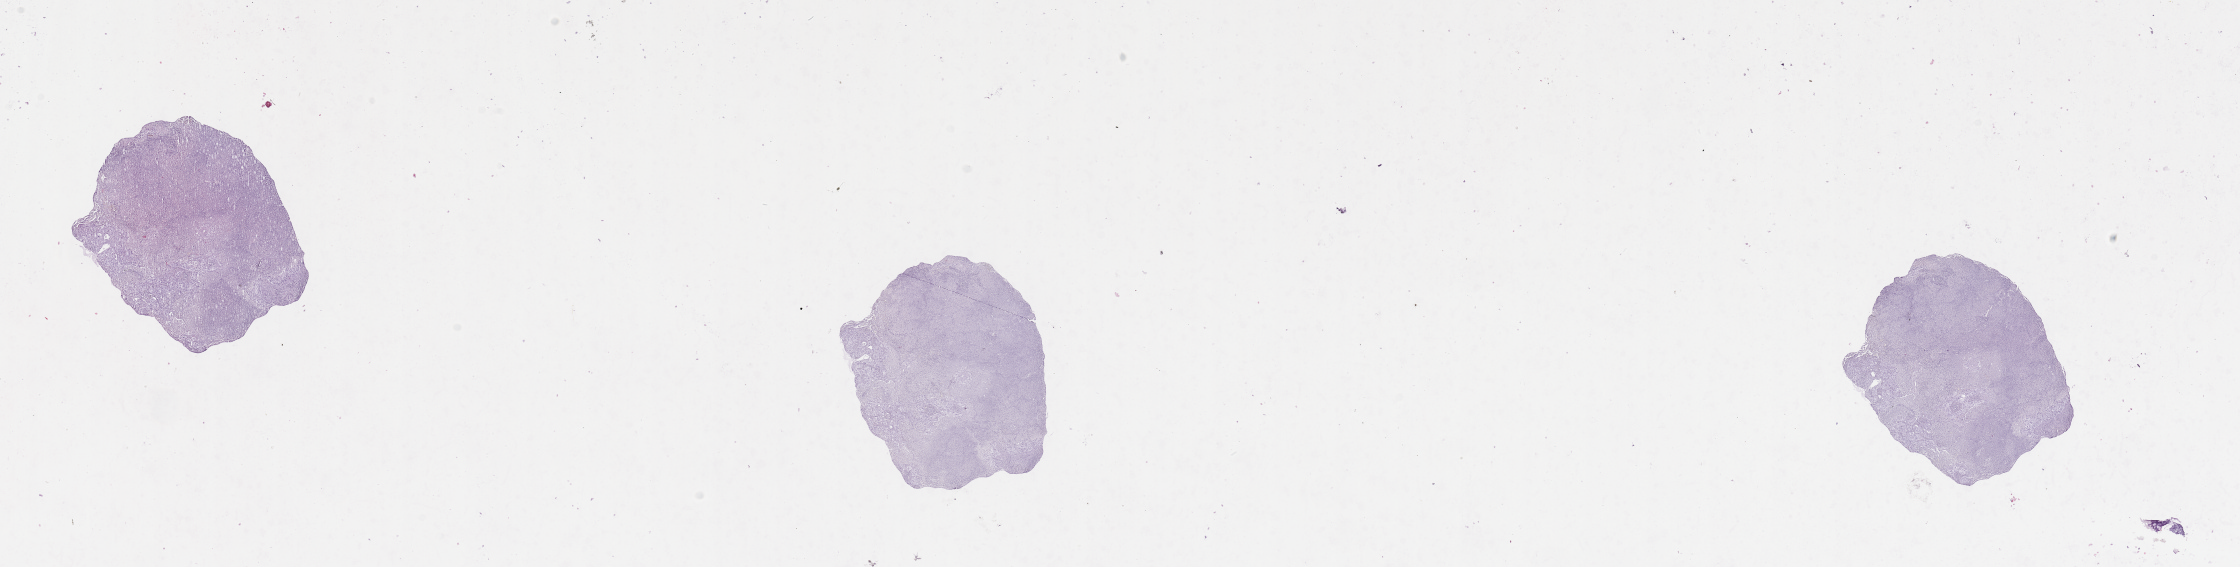
H&E-stained whole-slide image — low-resolution overview of the scanned area, about 35.4 x 9.0 mm (acquisition: 20x scan); lung, tumour tissue. Male, 74 y/o.
Diagnosis: Squamous cell carcinoma, NOS.